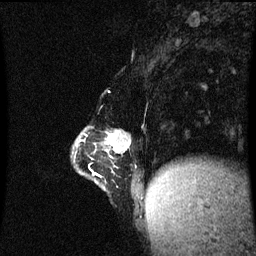
Breast MRI (dynamic contrast-enhanced), one sagittal slice; slice 19 of 60 in the series (ordered by position); dynamic contrast-enhanced series, image 2 of 3 at this slice position (ordered by acquisition); 1.5 T; TE 4.2 ms, TR 8.9 ms; 256 × 256 image matrix. Female patient, age 47 years. From the clinical record (not read from this slice): setting: breast cancer imaged before/during neoadjuvant chemotherapy; receptor status: HR-positive, HER2-negative.
Structures marked on this image (semi-automatic segmentation, software-assisted and operator-edited):
- analysis volume of interest (the breast-tissue region the enhancement analysis was run in; not a lesion): bounding box [x1, y1, x2, y2] px = [74, 128, 145, 197]
- tumour enhancement mask (voxels above the 70 % enhancement threshold inside the analysis volume of interest): [96, 134, 130, 175]